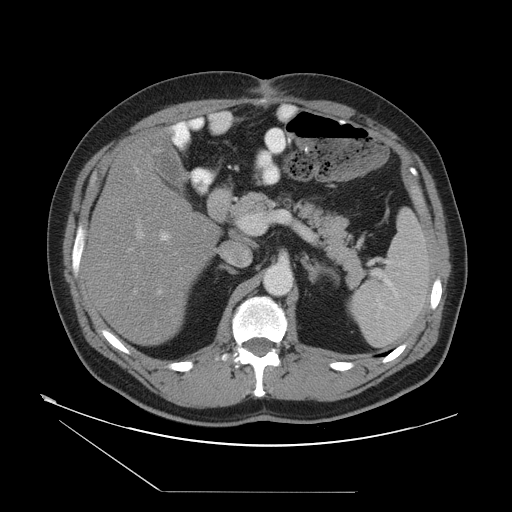
Contrast-enhanced abdominal CT, one axial slice; slice 26 of 55 in the series (ordered by position); intravenous contrast given; soft-tissue window (W 400 / L 40 HU); 5 mm slice thickness; 512 × 512 image matrix, field of view 454 × 454 mm. Male patient, age 59 years. From the clinical record (not read from this slice): diagnosis: colorectal cancer liver metastases, imaged before liver resection; multiple liver metastases: yes; largest metastasis: 0.3 cm; disease in both lobes: yes.
Structures marked on this image (manually delineated by an expert):
- hepatic veins: bounding box (x1, y1, x2, y2) in pixels: (127, 150, 175, 326)
- liver: (86, 137, 217, 347)
- planned liver remnant (the part of the liver to remain after resection): (85, 139, 218, 347)
- portal vein (with intrahepatic branches): (156, 233, 170, 295)